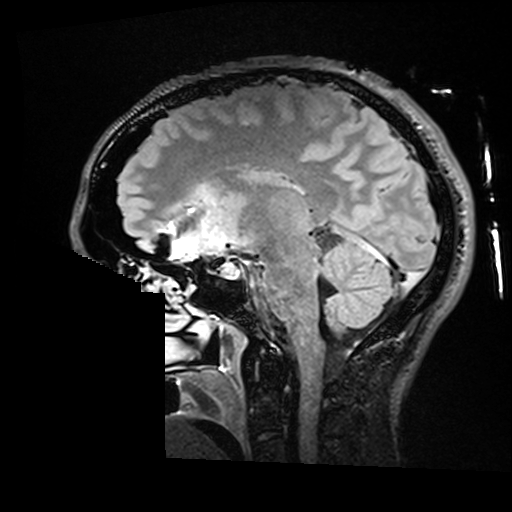
Brain MRI from a brain-tumour surgery series, one sagittal slice; slice 93 of 176 in the series (ordered by position); T2 FLAIR; 1 mm slice thickness; 512 × 512 image matrix. From the clinical record (not read from this slice): histopathology: Astrocytoma; WHO grade: 2; IDH mutation: yes; tumour location: Right Insular.
Outlined on this slice (expert manual segmentation):
- residual tumour: bounding box [x1, y1, x2, y2] px = [202, 184, 217, 203]